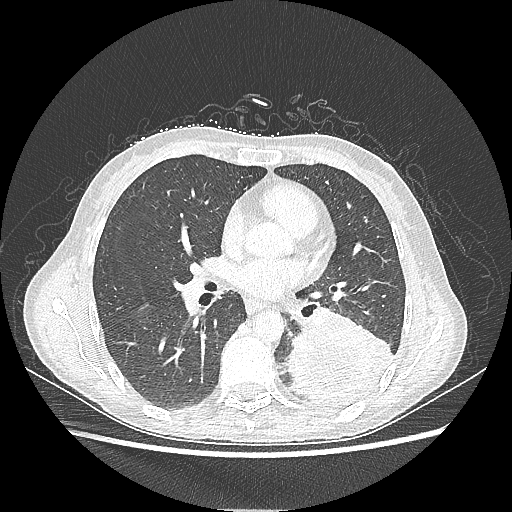
Chest CT, one axial slice. Position 113 of 220 along the scan axis. Lung window (W 1500 / L -600 HU). 1.25 mm slice thickness. 512 × 512 image matrix, field of view 360 × 360 mm. Female patient, age 53 years. From the clinical record (not read from this slice): clinical TNM (as recorded): T3 N0 M0.
Structures marked on this image (rectangle marked by the reading radiologist):
- lung tumour (recorded histology: adenocarcinoma): bounding box (x1, y1, x2, y2) in pixels: (284, 308, 395, 416)